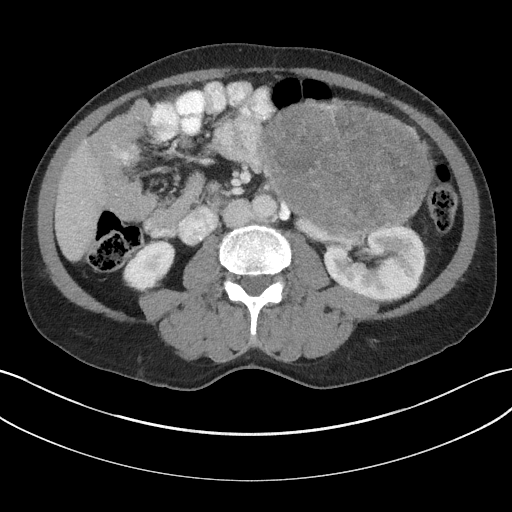
Contrast-enhanced abdominal CT, one axial slice; slice 82 of 147 in the series (ordered by position); reconstruction kernel I31f/3; soft-tissue window (W 400 / L 40 HU); 3 mm slice thickness; 512 × 512 image matrix, field of view 384 × 384 mm. Patient: male, 58 years. Case-level facts recorded for this patient, not image findings: diagnosis: adrenocortical carcinoma; tumour side: left adrenal; tumour size at pathology: 22 cm; Ki-67 index: 26 %; stage (as recorded): 2.
Outlined on this slice (semi-automatic segmentation, software-assisted and operator-edited):
- mass: bounding box [x1, y1, x2, y2] px = [262, 106, 428, 231]